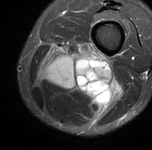
MRI of an extremity soft-tissue mass, one axial slice; position 28 of 90 along the scan axis; STIR; MR volume resampled by the dataset authors to the PET/CT grid (not the native acquisition matrix); 3.27 mm slice thickness; 152 × 150 image matrix. Male patient. Case-level facts recorded for this patient, not image findings: histological type: undifferentiated pleomorphic liposarcoma; grade: high; site of the primary tumour: left thigh.
Outlined on this slice (expert contour drawn on MRI and transferred to this co-registered scan by the dataset authors):
- gross tumour volume including surrounding oedema: box from (x=38, y=41) to (x=119, y=120) px
- gross tumour volume (mass): (x=77, y=80)–(x=90, y=90)